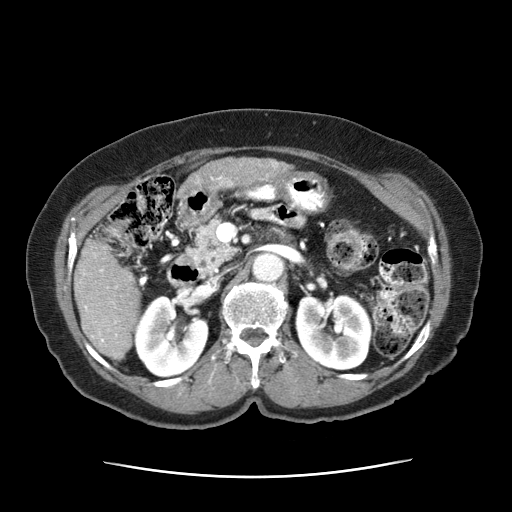
Contrast-enhanced abdominal CT (liver protocol), one axial slice. Slice 18 of 63 in the series (ordered by position). 120 kVp. Intravenous contrast given. Soft-tissue window (W 400 / L 40 HU). 2.5 mm slice thickness. 512 × 512 image matrix, field of view 360 × 360 mm. Patient: female, 79 years. Case-level facts recorded for this patient, not image findings: diagnosis: hepatocellular carcinoma (patient treated with transarterial chemoembolisation; whether this scan precedes or follows treatment is not stated here); TNM stage (as recorded): Stage-II; Child-Pugh class: B; tumour differentiation: well differentiated; tumour nodularity: multinodular.
Outlined on this slice (semi-automatically segmented with operator editing):
- abdominal aorta: bounding box <253,251,284,281> (left, top, right, bottom; pixels)
- liver parenchyma outside the tumour (the mass and vessels are separate outlines, so this box may not span the whole liver): <74,240,144,363>
- mass: <177,160,291,195>
- liver vessels: <84,269,131,343>